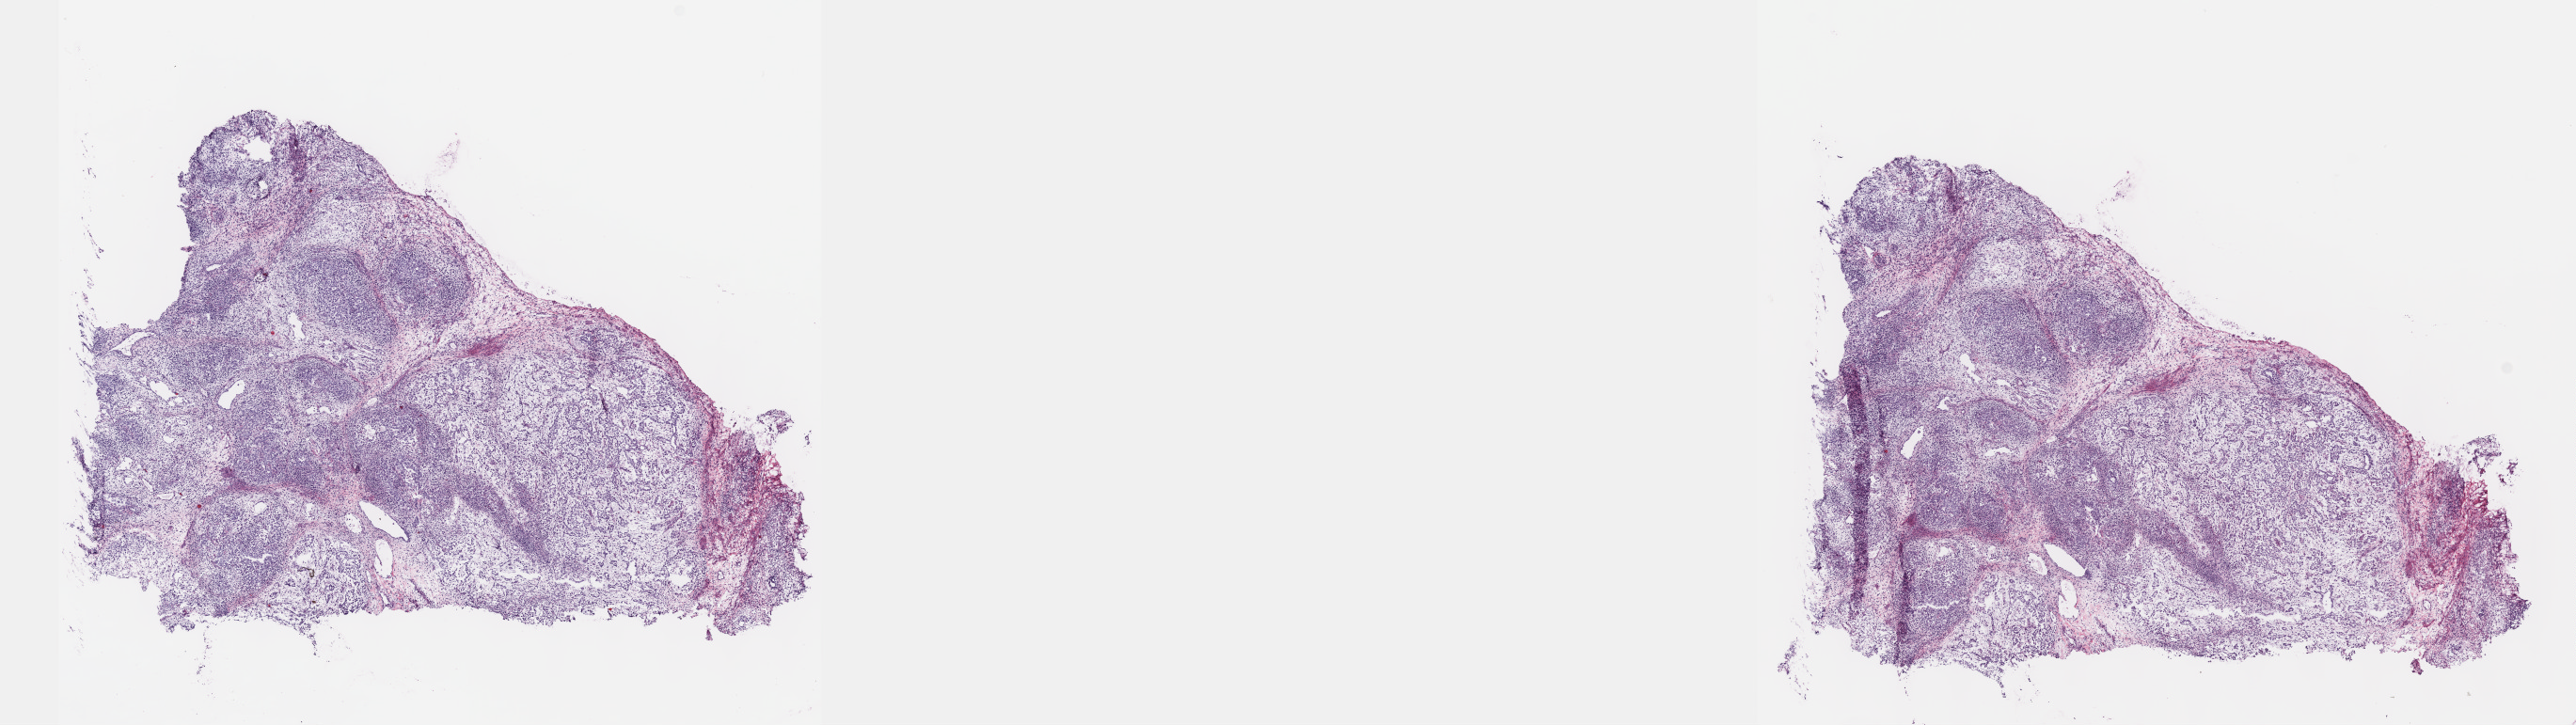
Digitized Hematoxylin and eosin (H&E) stained tissue section (whole slide) — whole scanned area (about 22.1 x 6.2 mm, slide scanned at 40x) shown as a low-resolution overview; frozen section; primary tumour sample from the testis. Patient: male, age at initial diagnosis 26 years. Slide review estimates, as recorded: tumour cells 100%, tumour nuclei 75%, normal cells 0%, stromal cells 0%, necrosis 0%. Infiltration values recorded for this section: lymphocyte infiltration 3%, monocyte infiltration 0%, neutrophil infiltration 0%.
- pathologic diagnosis: Mixed germ cell tumor
- laterality: left